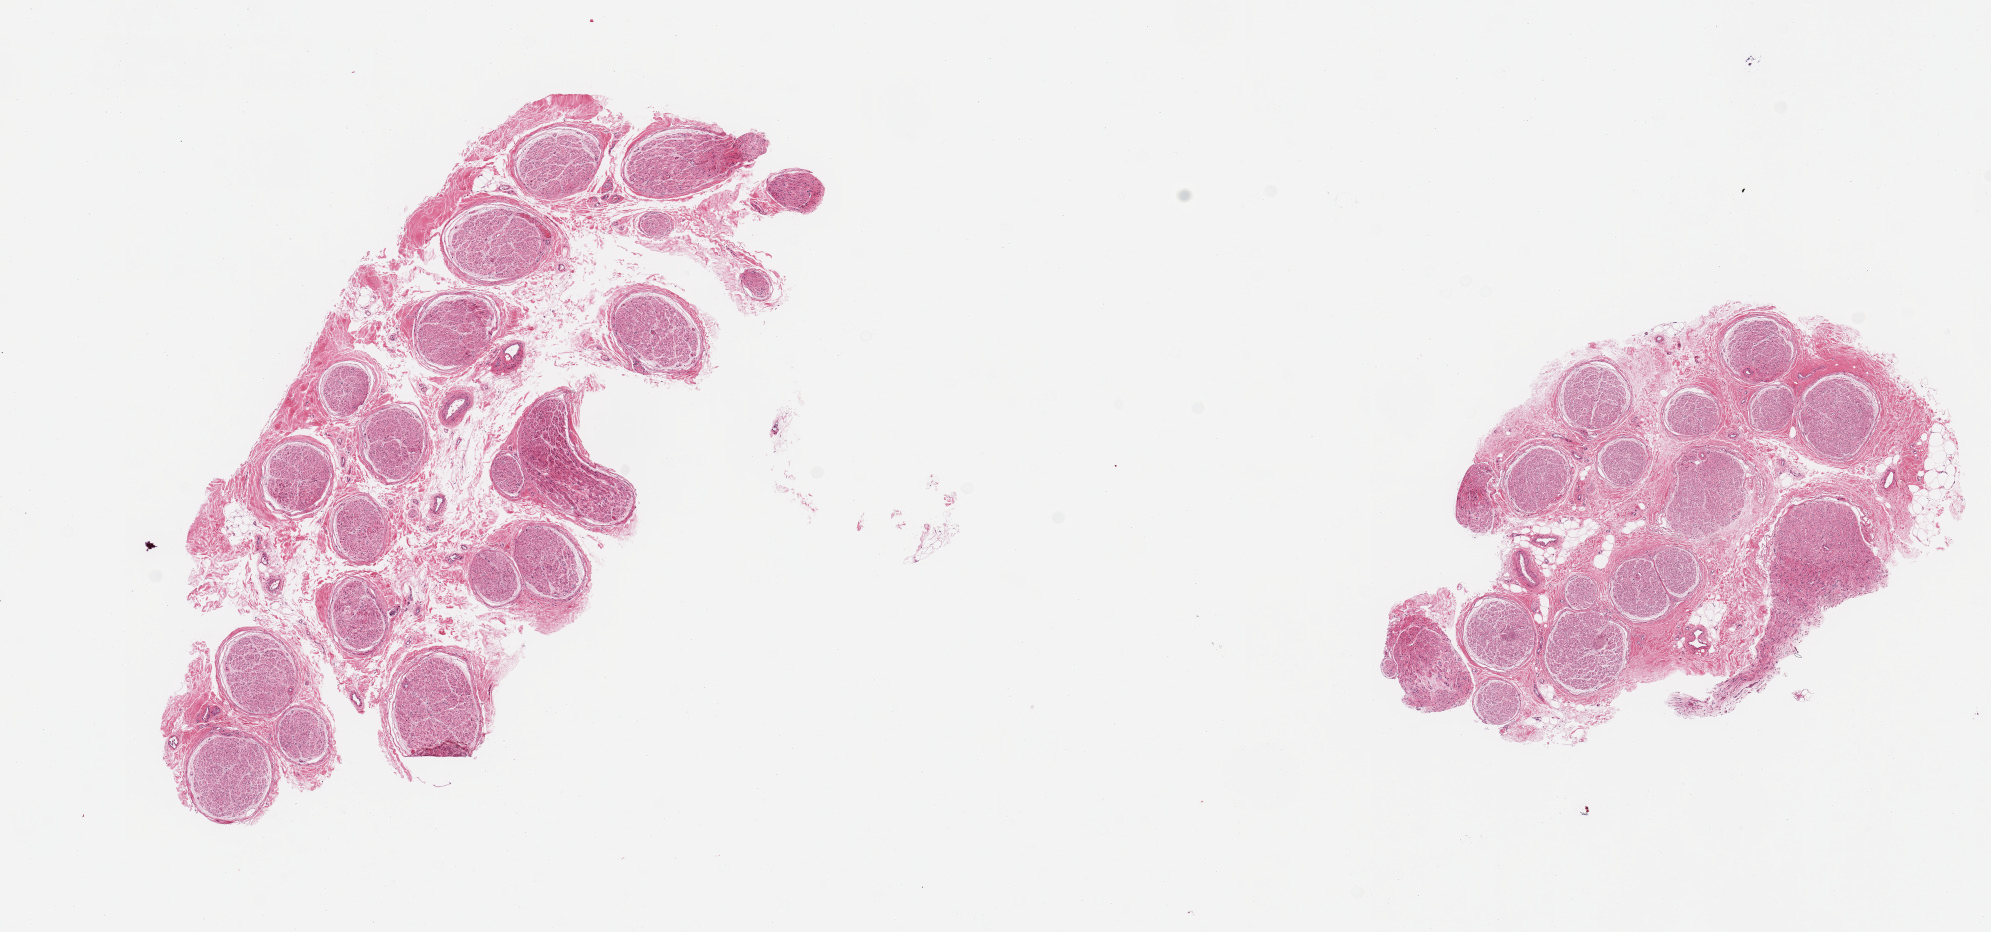
Whole-slide image, haematoxylin and eosin stain, shown as a low-resolution overview of the whole scanned area (about 15.8 x 7.4 mm, slide scanned at 20x). PAXgene-fixed, paraffin-embedded tissue. Sampled site (target tissue): tibial nerve. Donor tissue sample. Donor sex: male.
Reviewer comment on this tissue sample: 2 pieces, minimal adherent fat.